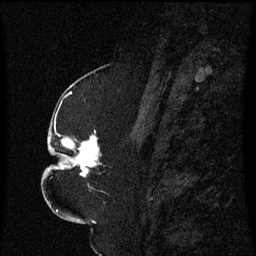
Breast MRI (dynamic contrast-enhanced), one sagittal slice; dynamic contrast-enhanced series, image 2 of 3 at this slice position (ordered by acquisition); 1.5 T; TE 4.2 ms, TR 8.4 ms; 2.3 mm slice thickness; 256 × 256 image matrix, field of view 200 × 200 mm. Female patient, age 52 years. From the clinical record (not read from this slice): setting: breast cancer imaged before/during neoadjuvant chemotherapy; receptor status: HR-positive, HER2-negative.
Structures marked on this image (semi-automatically segmented with operator editing):
- analysis volume of interest (the breast-tissue region the enhancement analysis was run in; not a lesion): box from (x=49, y=124) to (x=112, y=193) px
- tumour enhancement mask (voxels above the 70 % enhancement threshold inside the analysis volume of interest): (x=49, y=136)–(x=100, y=177)